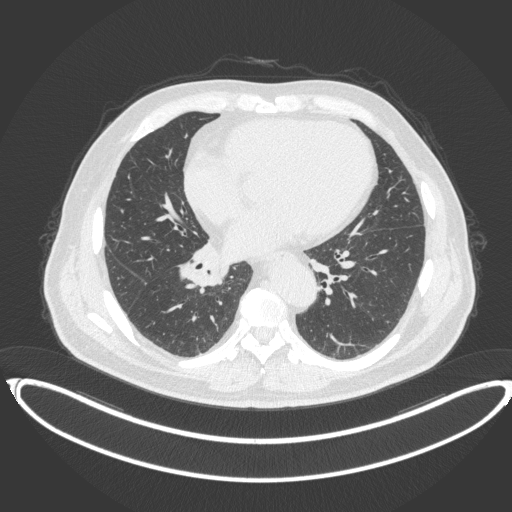
Chest CT, one axial slice; position 173 of 383 along the scan axis; reconstruction kernel B31f; 120 kVp; lung window (W 1500 / L -600 HU); 512 × 512 image matrix, field of view 448 × 448 mm. Patient: male, 61 years. From the clinical record (not read from this slice): clinical TNM (as recorded): T1b N1 M0.
Structures marked on this image (bounding box drawn by a radiologist):
- lung tumour (recorded histology: squamous cell carcinoma): bounding box <173,243,229,292> (left, top, right, bottom; pixels)